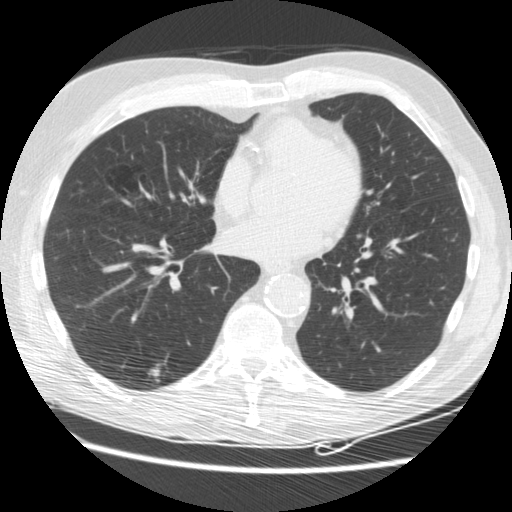
Low-dose screening chest CT, one axial slice. Position 76 of 176 along the scan axis. Reconstruction kernel STANDARD. Lung window (W 1500 / L -600 HU). 2.5 mm slice thickness. 512 × 512 image matrix, field of view 347 × 347 mm.
Annotated regions visible in this slice (manually delineated by an expert):
- lesion 2 (tumor, lower lobe of right lung): bounding box (x1, y1, x2, y2) in pixels: (149, 367, 159, 377)